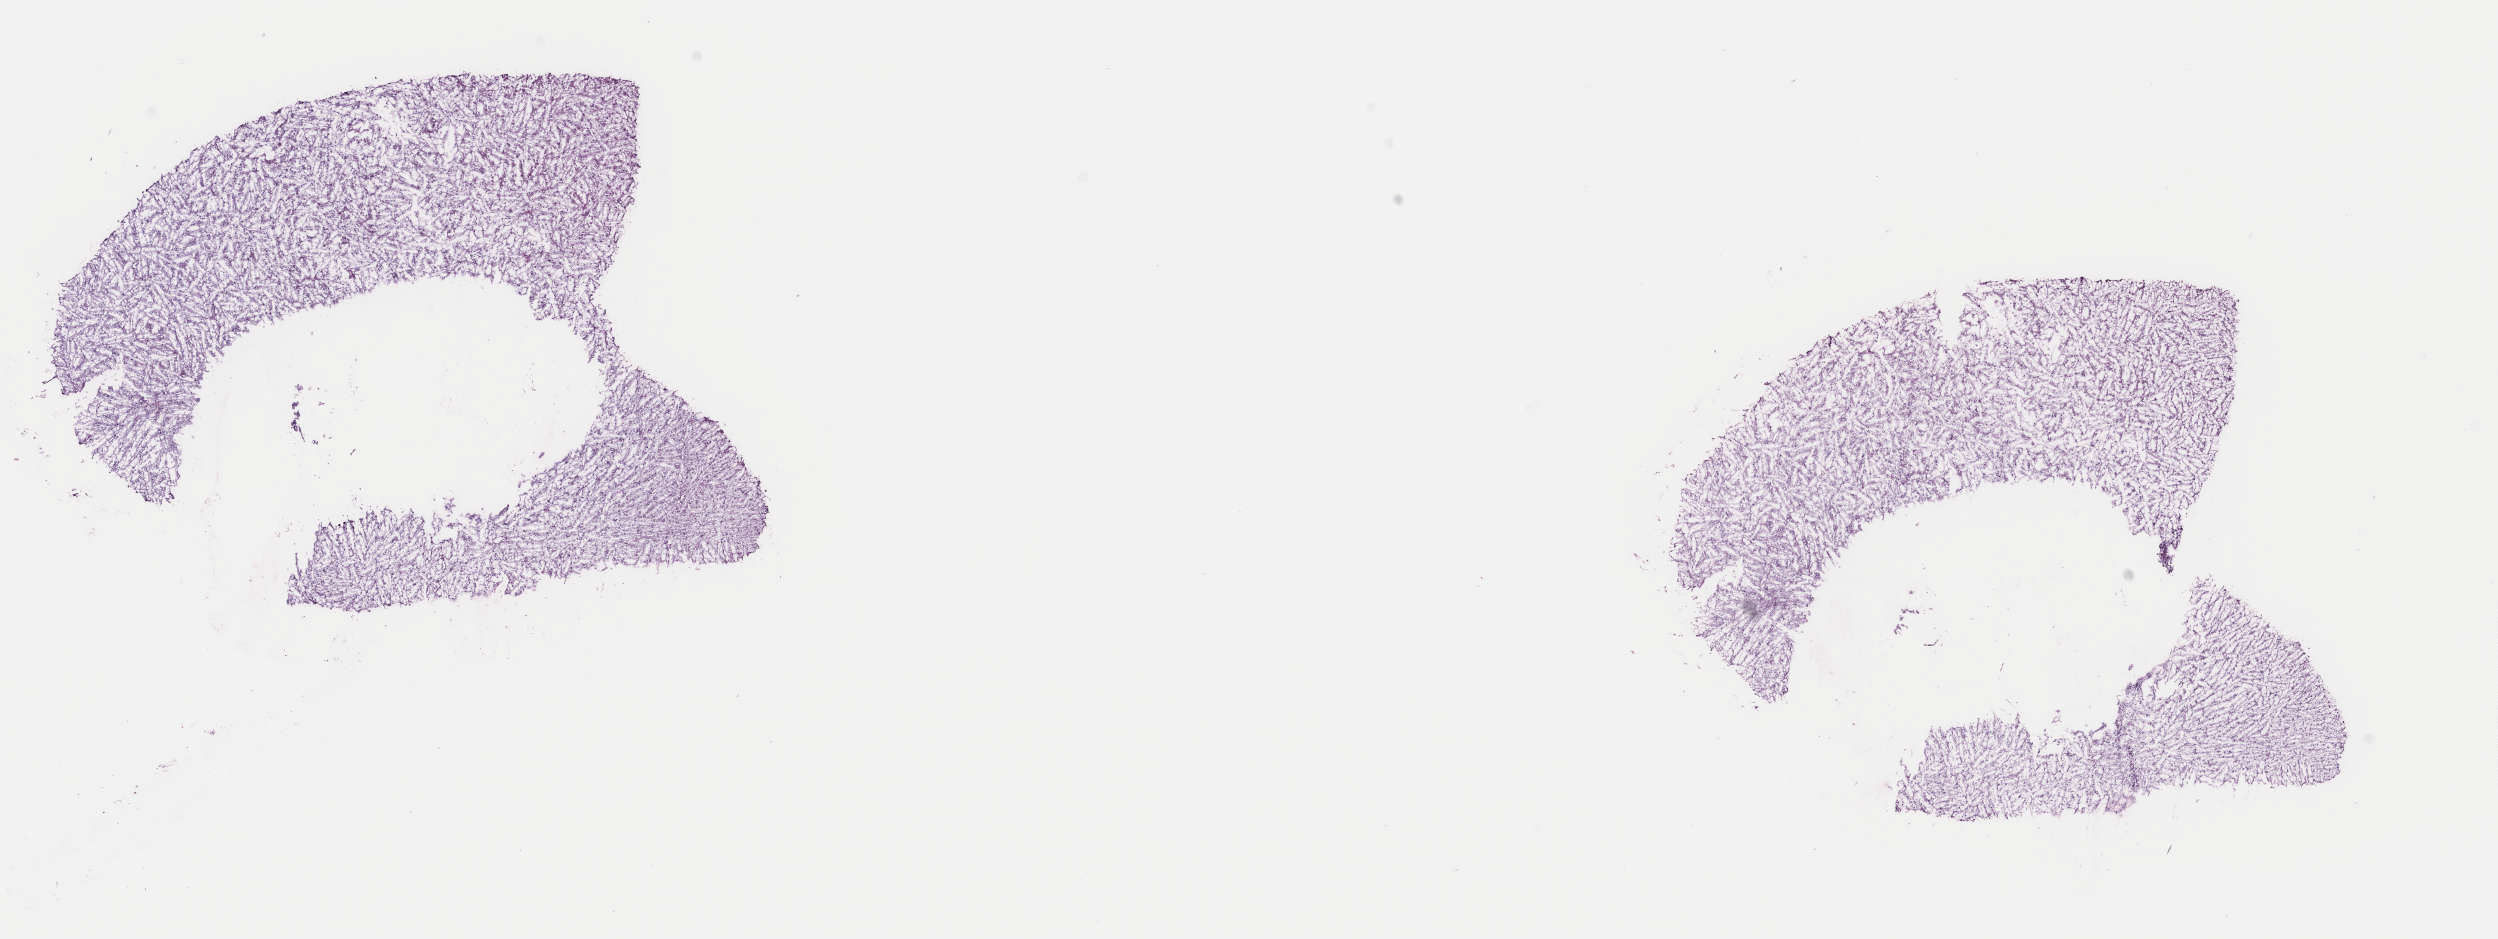
Whole-slide histology image, H&E, shown as a low-resolution overview of the whole scanned area (about 19.8 x 7.5 mm, slide scanned at 40x); frozen section from the top of the tissue portion; primary tumour sample from the brain. Female, age 48 years at initial diagnosis. Histologic grade: G3 (poorly differentiated). Slide review estimates, as recorded: tumour cells 70%, tumour nuclei 90%, normal cells 5%, stromal cells 25%, necrosis 0%. Infiltration values recorded for this section: lymphocyte infiltration 0%, monocyte infiltration 0%, neutrophil infiltration 0%.
* pathologic diagnosis: Astrocytoma, anaplastic (cerebrum)